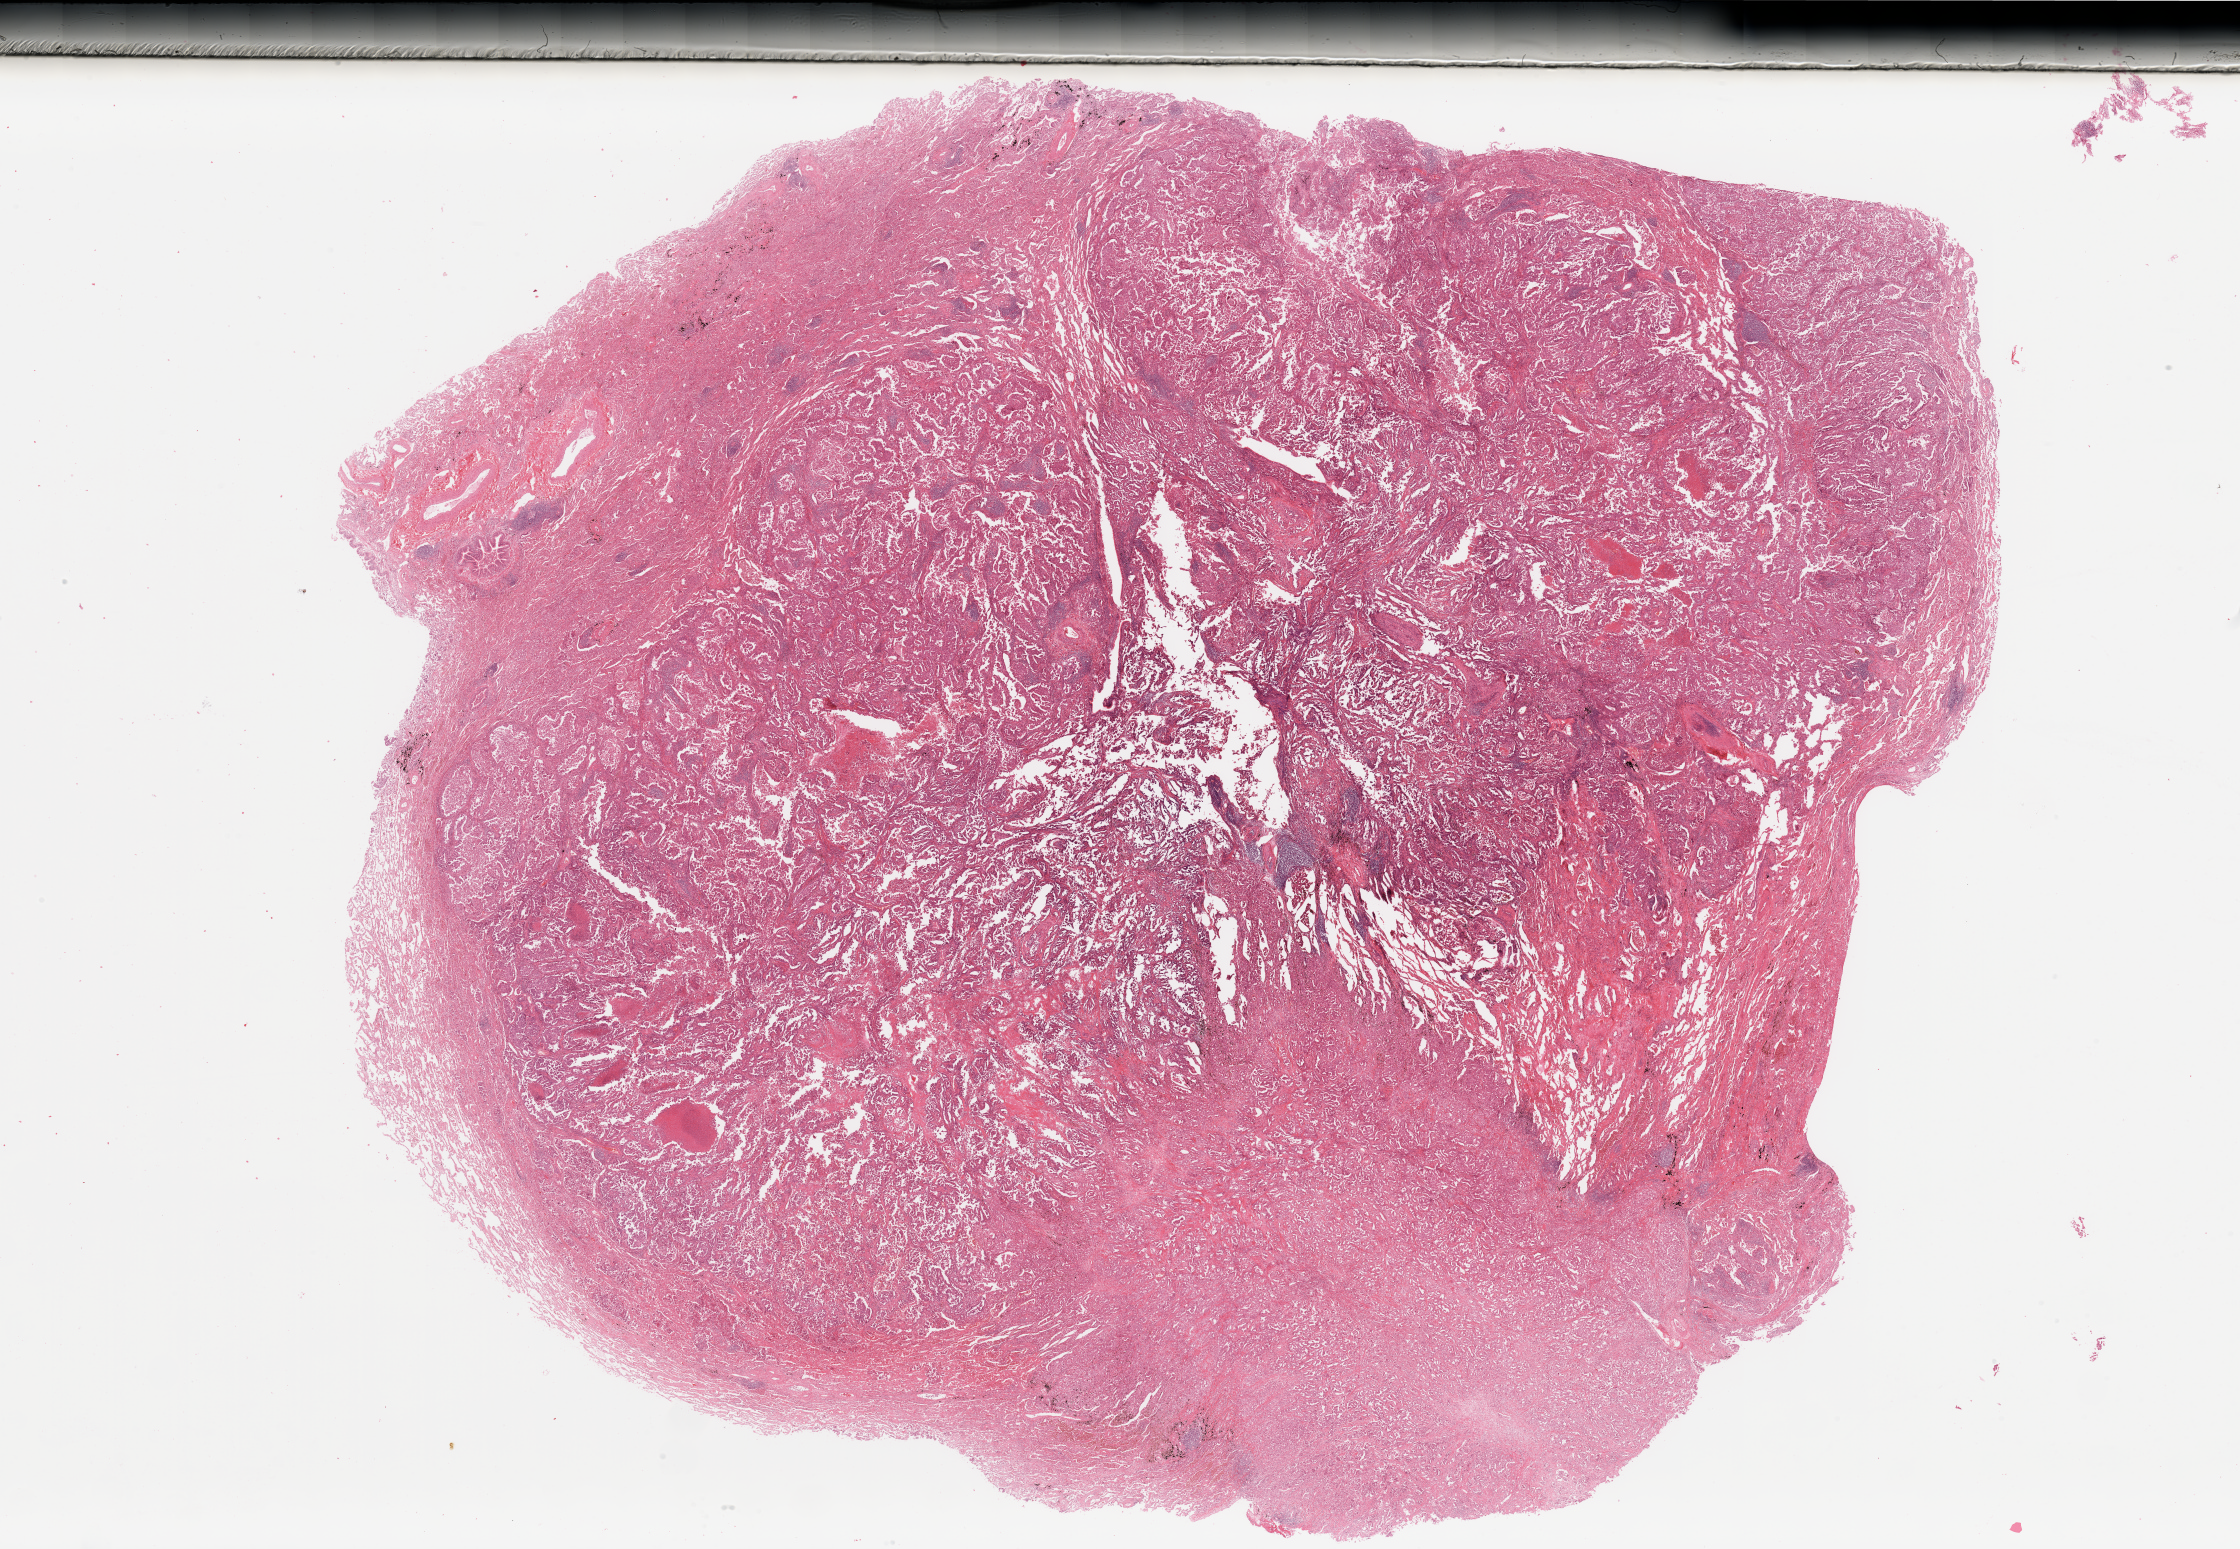
Hematoxylin and eosin (H&E) stained whole-slide image, whole scanned area (about 35.4 x 24.5 mm, slide scanned at 20x) shown as a low-resolution overview. Tumour tissue sample, lung. Patient: male, age 59 years. Histologic grade: G2 (moderately differentiated).
Histologic diagnosis: Adenocarcinoma, NOS. AJCC pathologic stage: IIIA.